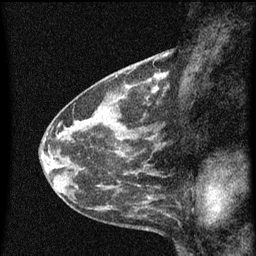
Breast MRI (dynamic contrast-enhanced), one sagittal slice; dynamic contrast-enhanced series, image 2 of 3 at this slice position (ordered by acquisition); 1.5 T; TE 4.2 ms, TR 8 ms; 2 mm slice thickness; 256 × 256 image matrix. Patient: female, 41 years.
Outlined on this slice (semi-automatically segmented with operator editing):
- analysis volume of interest (the breast-tissue region the enhancement analysis was run in; not a lesion): bounding box [x1, y1, x2, y2] px = [130, 76, 157, 103]
- tumour enhancement mask (voxels above the 70 % enhancement threshold inside the analysis volume of interest): [136, 76, 157, 99]